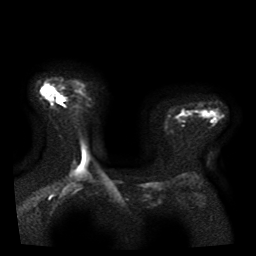
Breast MRI, one axial slice. Position 28 of 41 along the scan axis. Diffusion-weighted series; image 2 of 4 stored at this slice position (different b-values; order by instance number). 1.5 T. 5 mm slice thickness. 256 × 256 image matrix. Female patient.
Structures marked on this image (manually delineated by an expert):
- tumour on diffusion-weighted imaging: box from (x=55, y=93) to (x=60, y=96) px